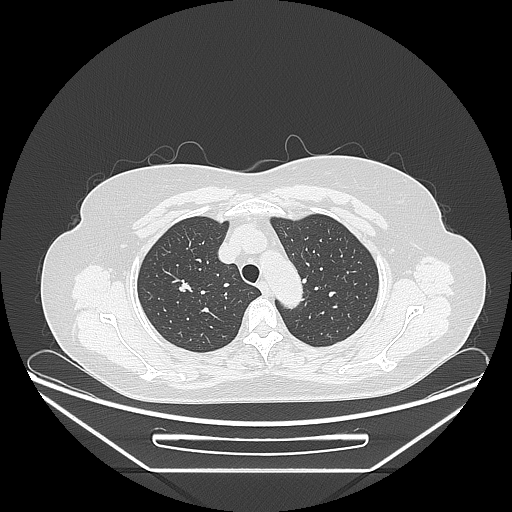
Chest CT, one axial slice; 120 kVp; lung window (W 1500 / L -600 HU); 512 × 512 image matrix, field of view 433 × 433 mm. Female patient, age 60 years. From the clinical record (not read from this slice): clinical TNM (as recorded): T1c N0 M0.
Outlined on this slice (rectangle marked by the reading radiologist):
- lung tumour (recorded histology: adenocarcinoma): bounding box (x1, y1, x2, y2) in pixels: (174, 275, 201, 303)